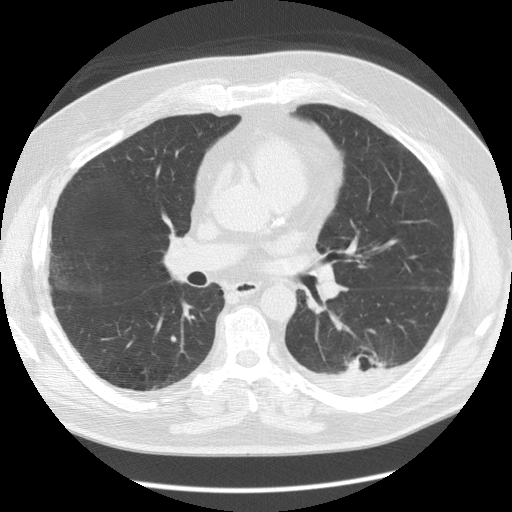
Chest CT (low-dose screening protocol), one axial image. Baseline screening round. Lung window (W 1500 / L -600 HU). Standard (soft-tissue) reconstruction kernel (STANDARD). 120 kVp. Male, age 56 years at enrolment. Former smoker at enrolment.
Expert reader's lesion annotation, bounding box [x1, y1, x2, y2] px = [323, 340, 395, 393]. The screening reader recorded 4 non-calcified nodules or masses ≥4 mm on this exam (left lower lobe, left lower lobe, right middle lobe, left upper lobe); which of them this box marks is not recorded. Official screen result: positive, change unspecified: nodule(s) >= 4 mm or enlarging nodule(s), mass(es), or other non-specific abnormalities suspicious for lung cancer.